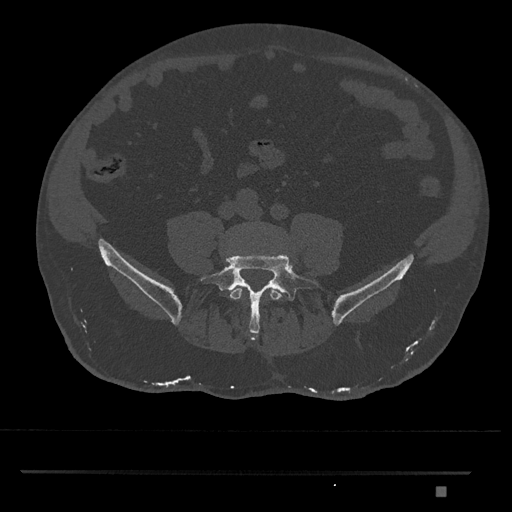
CT including the spine, one axial slice; slice 572 of 1134 in the series (ordered by position); reconstruction kernel Br40s/3; bone window (W 1800 / L 400 HU); 0.5 mm slice thickness; 512 × 512 image matrix, field of view 429 × 429 mm. Male patient, age 65 years. Case-level facts recorded for this patient, not image findings: primary cancer: prostate.
Outlined on this slice (semi-automatic segmentation, software-assisted and operator-edited):
- L4 vertebra: bounding box [x1, y1, x2, y2] px = [229, 287, 285, 300]
- L5 vertebra: [200, 253, 322, 337]